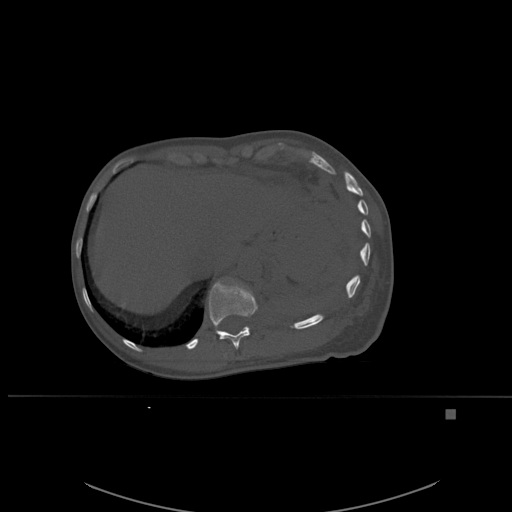
CT including the spine, one axial slice. Position 297 of 537 along the scan axis. Bone window (W 1800 / L 400 HU). 1.5 mm slice thickness. 512 × 512 image matrix, field of view 440 × 440 mm. Female patient, age 45 years. From the clinical record (not read from this slice): primary cancer: lung.
Annotated regions visible in this slice (semi-automatic segmentation, software-assisted and operator-edited):
- T11 vertebra: box from (x=209, y=278) to (x=258, y=349) px